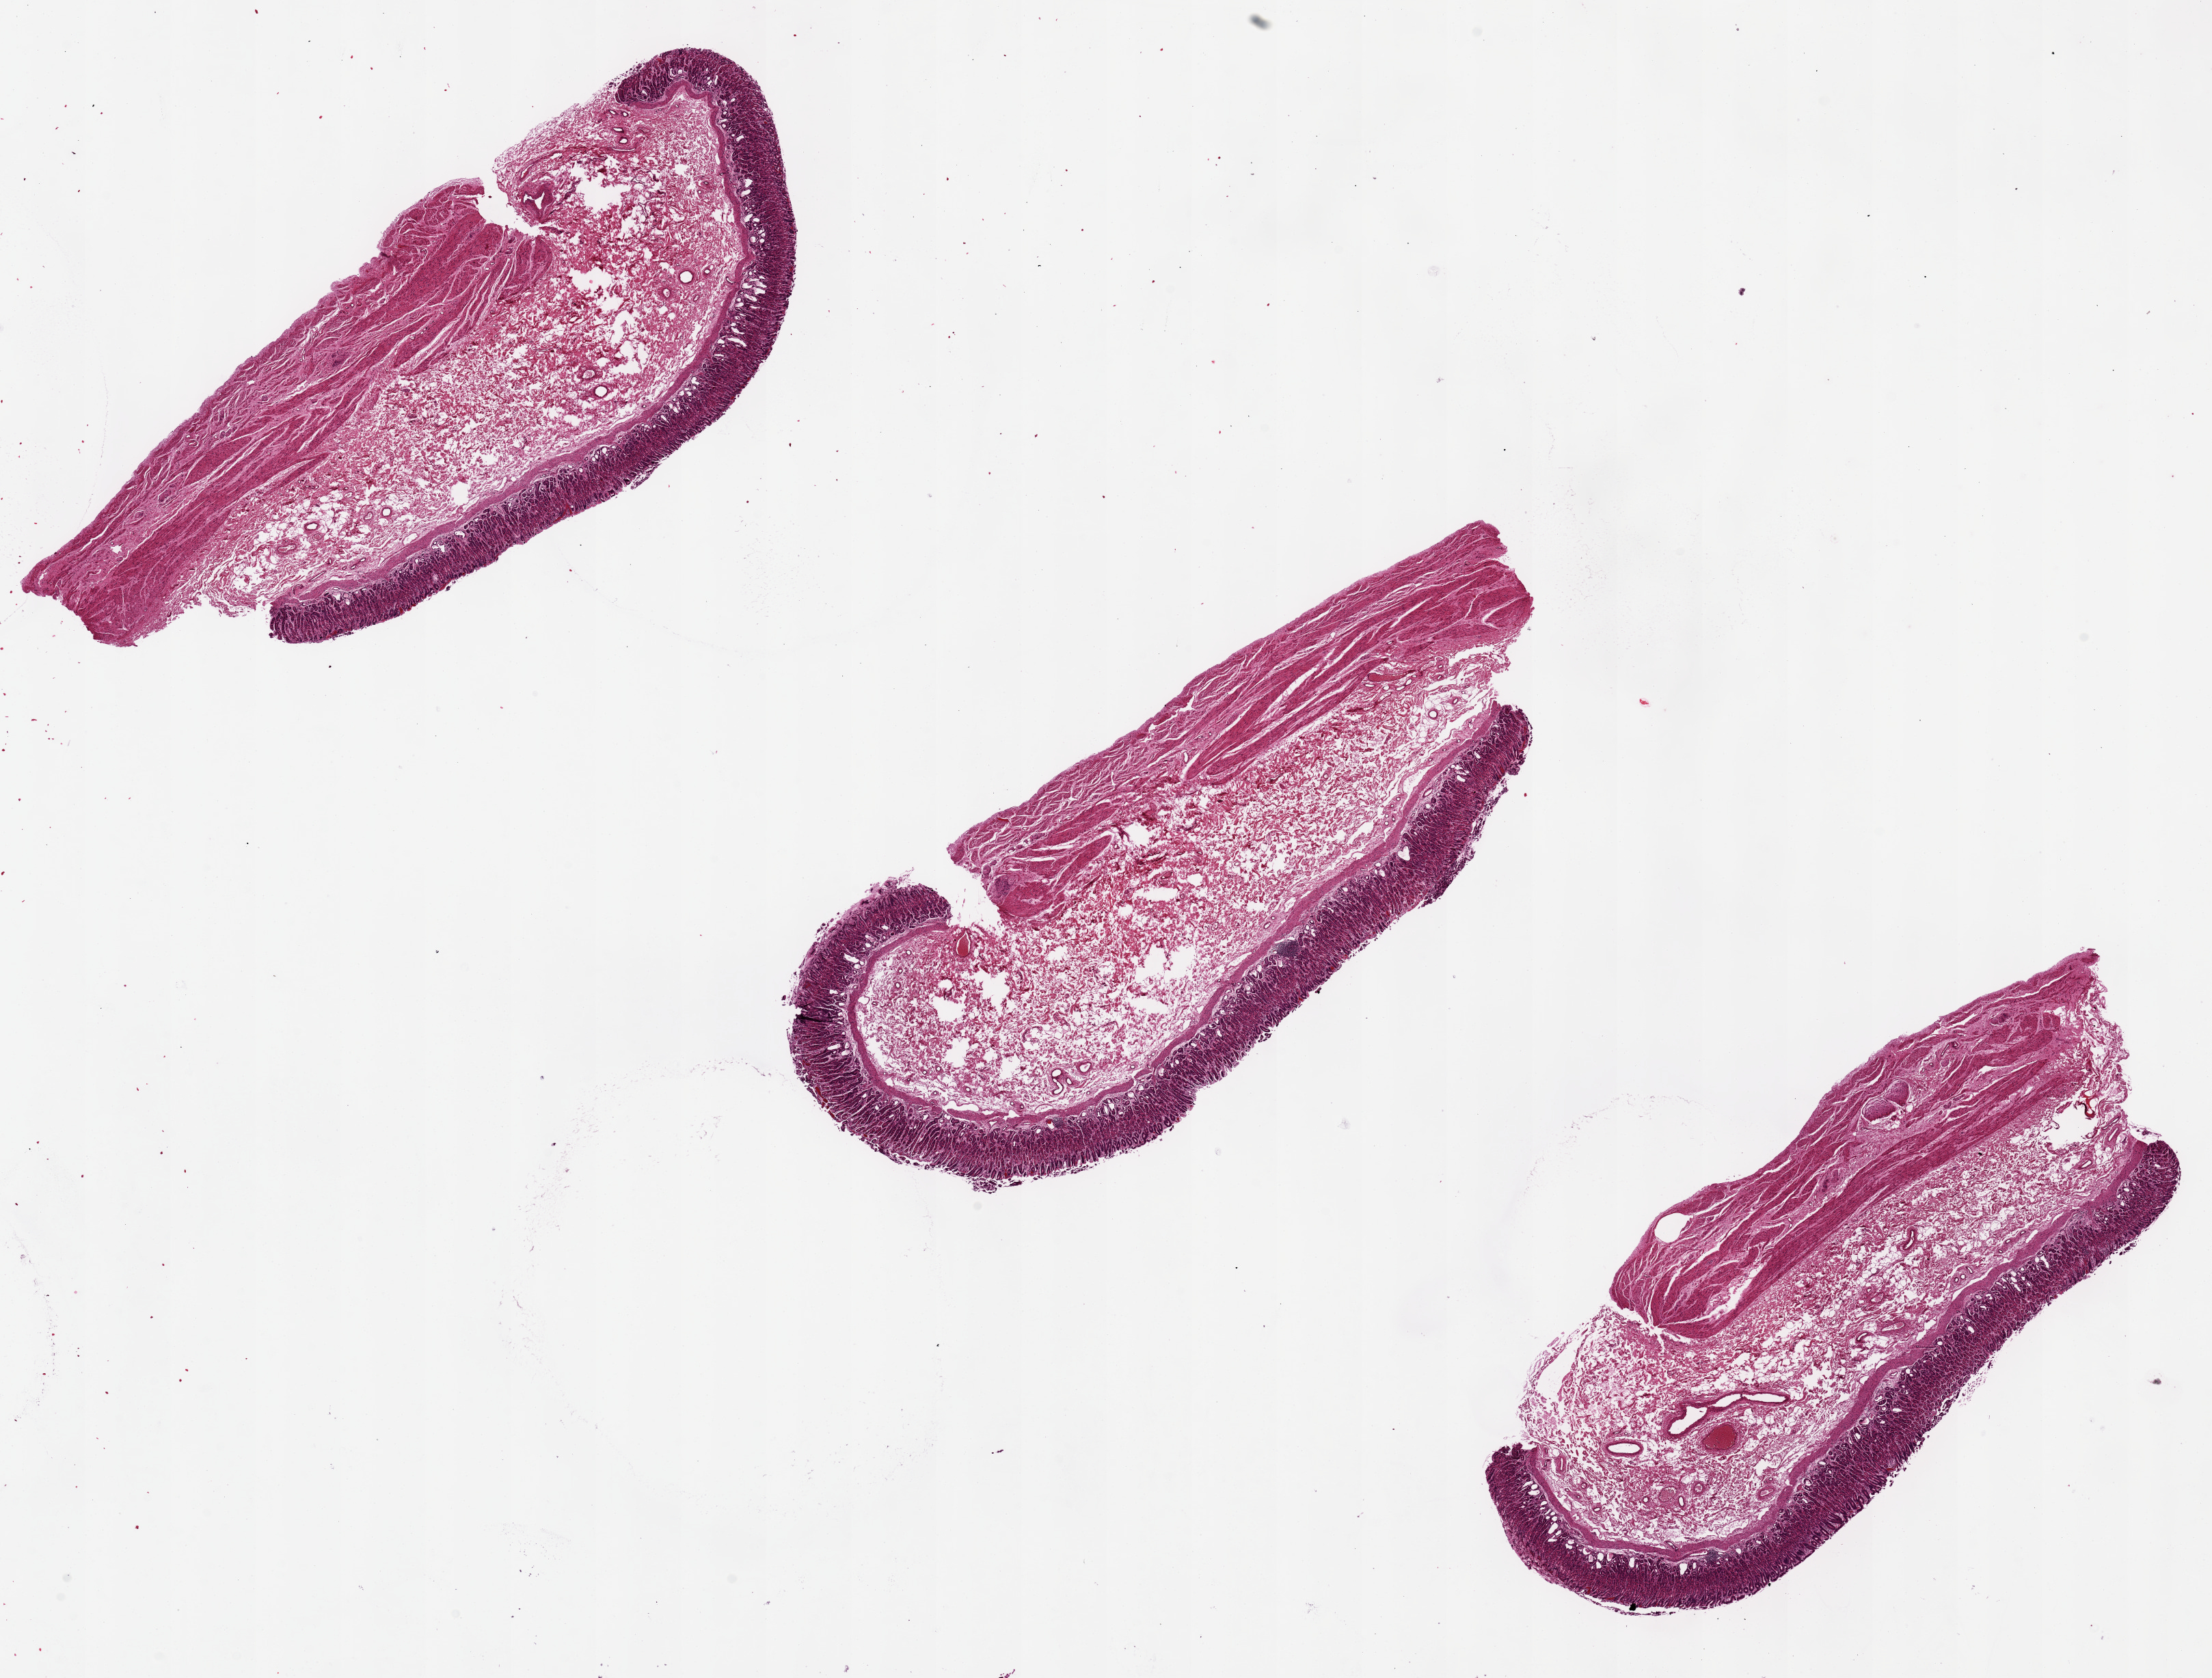
Hematoxylin and eosin (H&E) whole-slide image, low-resolution overview of the scanned area, about 25.6 x 19.4 mm (acquisition: 20x scan). PAXgene-fixed paraffin-embedded (PFPE) section. Sampled site (target tissue): stomach. Tissue donor sample. Donor: male.
• reviewer comment on this tissue sample: 3 pieces, 3.4 mm width; mucosa 0.7 mm thick; mild surface autolysis